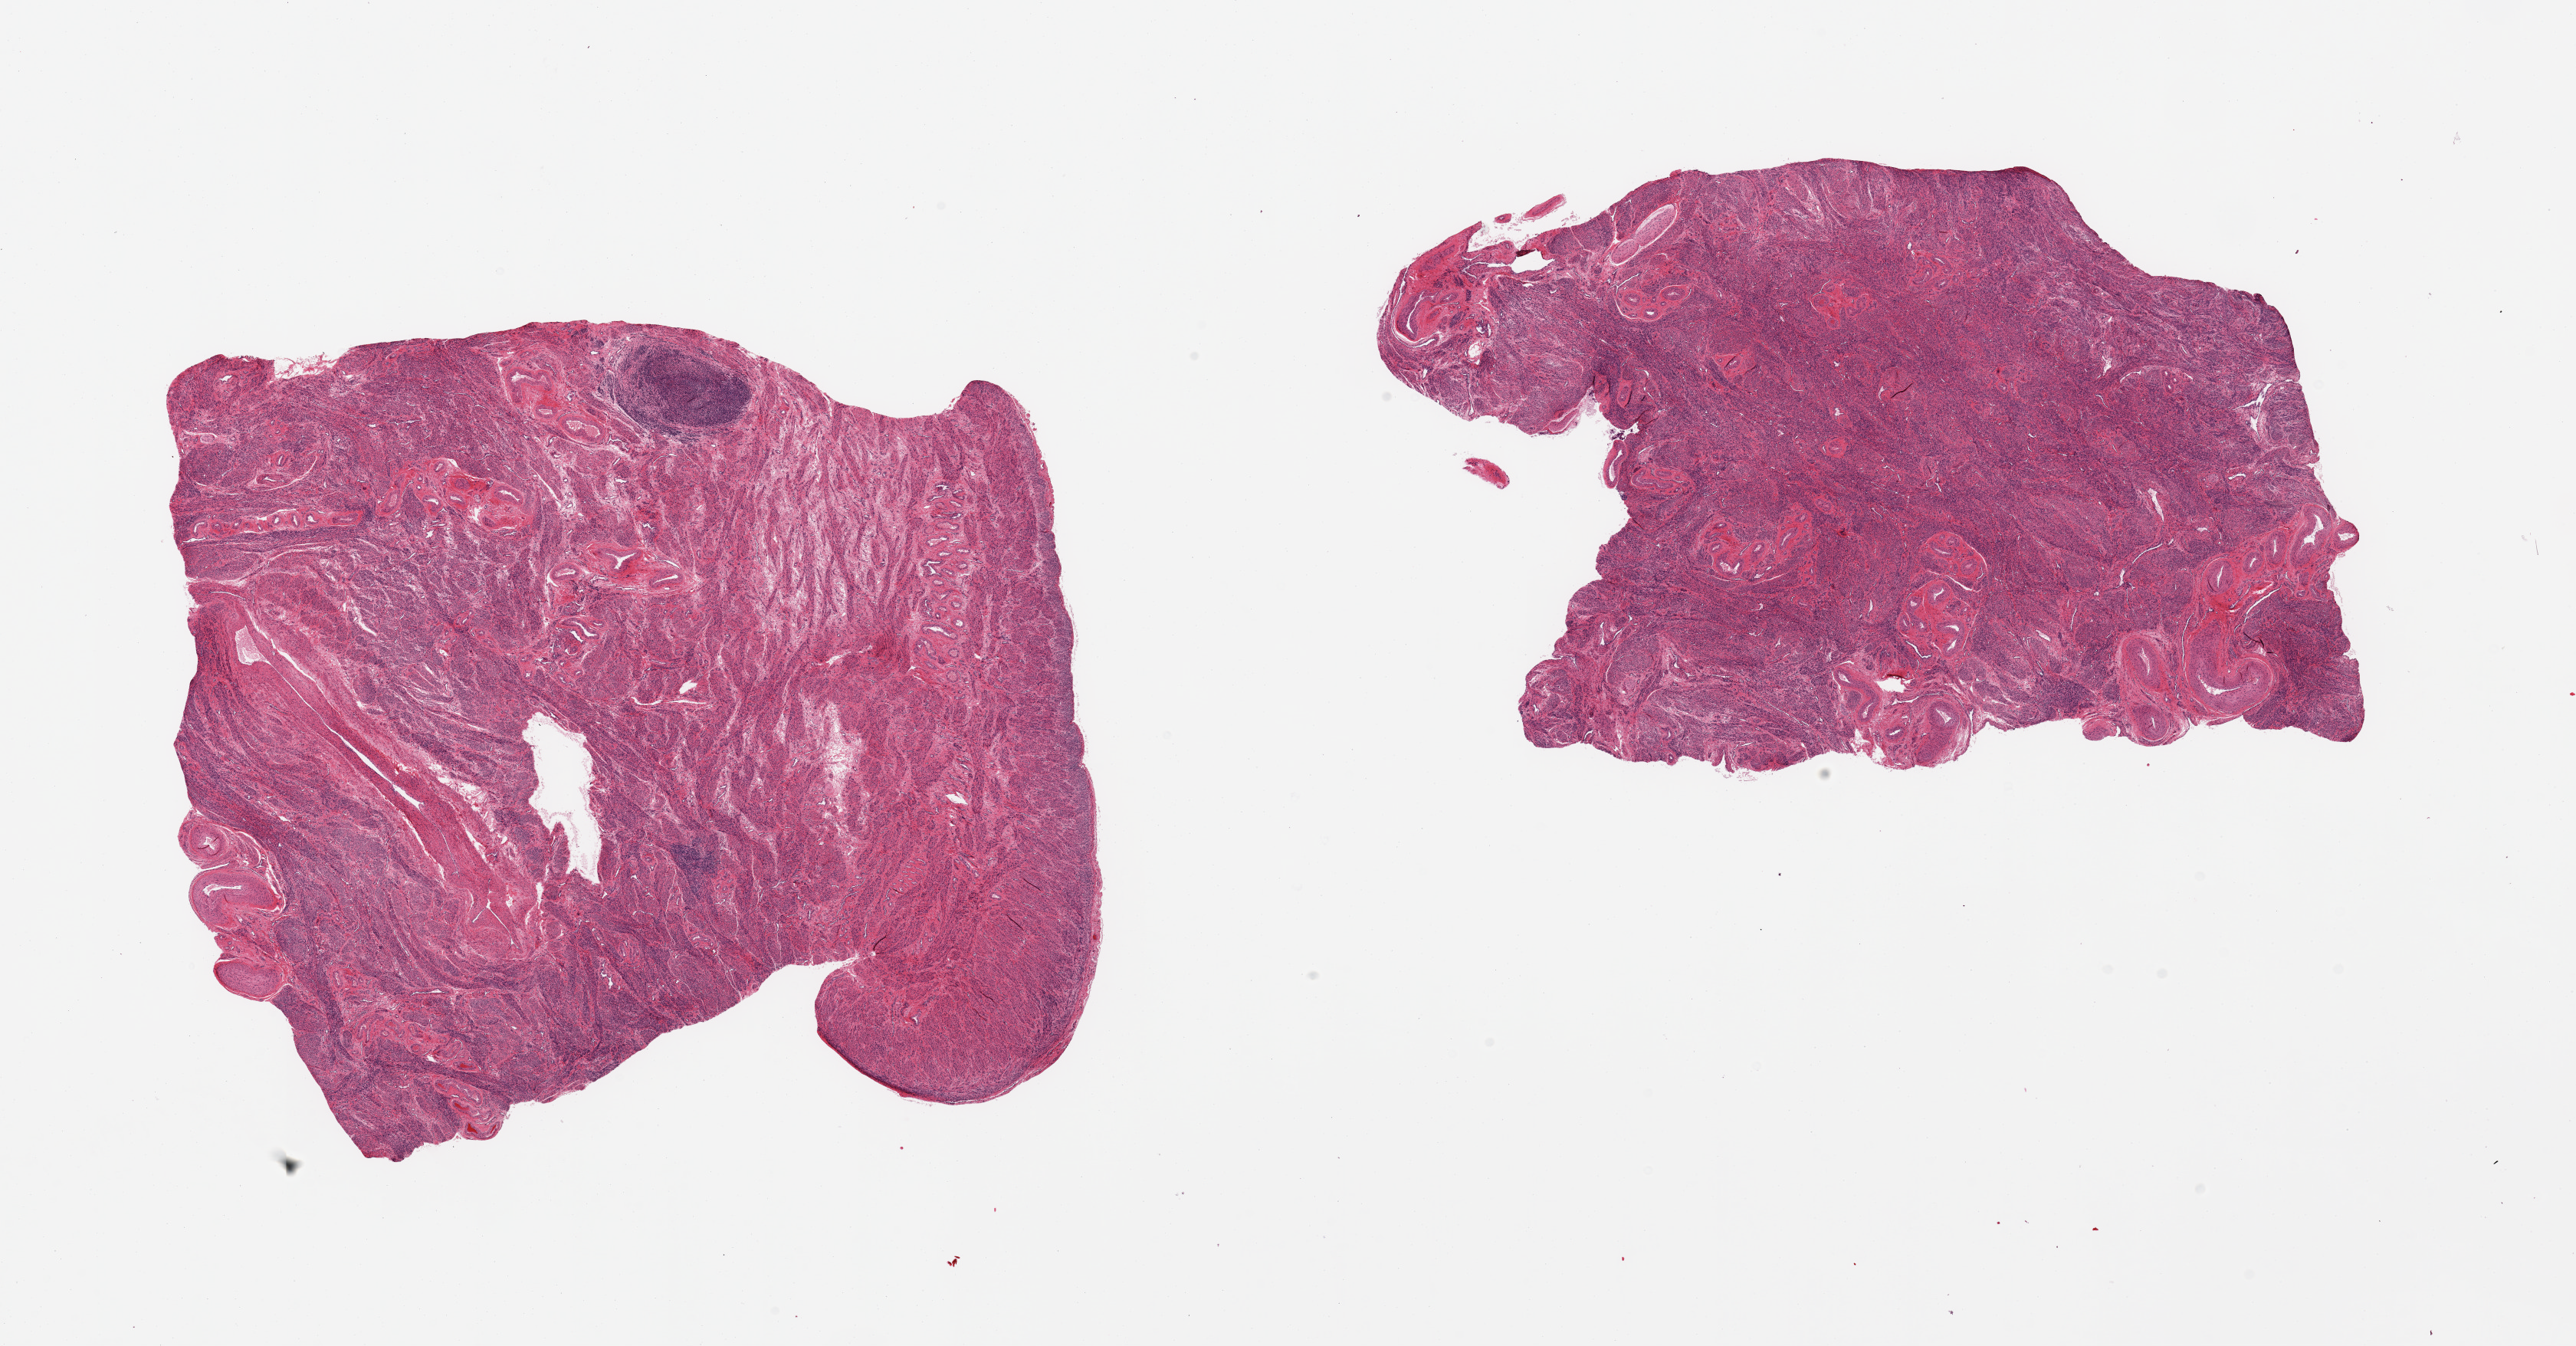
Whole-slide image, H&E stain — whole scanned area (about 26.6 x 13.9 mm, from a 20x scan) shown as a low-resolution overview, PAXgene-fixed, paraffin-embedded tissue, sampled site (target tissue): uterus, donor tissue sample. Donor: female.
Reviewer comment on this tissue sample: 2 pieces, myometrium; minute(~1mm)nodule of endometrial stroma.